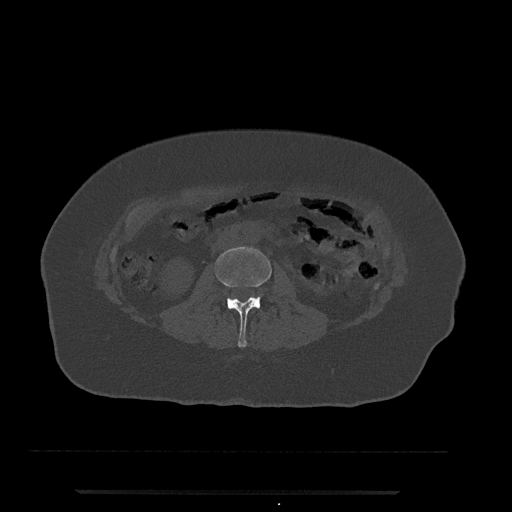
CT including the spine, one axial slice. Position 22 of 797 along the scan axis. 120 kVp. Bone window (W 1800 / L 400 HU). 512 × 512 image matrix, field of view 440 × 440 mm. Female patient, age 51 years. Case-level facts recorded for this patient, not image findings: primary cancer: neuro; vertebrae with lytic lesions (as recorded): T8.
Structures marked on this image (semi-automatically segmented with operator editing):
- L2 vertebra: bounding box (x1, y1, x2, y2) in pixels: (214, 247, 272, 347)